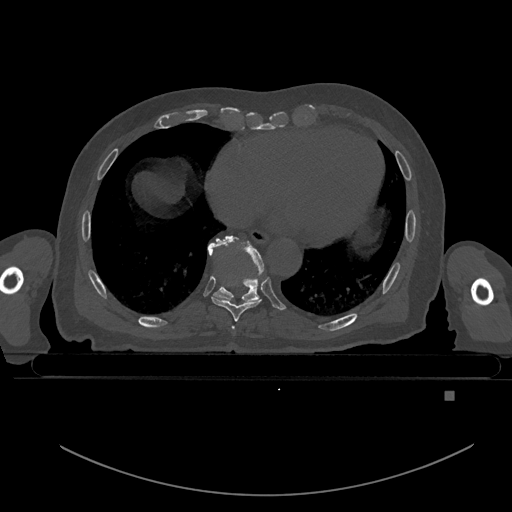
CT including the spine, one axial slice. Bone window (W 1800 / L 400 HU). 0.5 mm slice thickness. 512 × 512 image matrix, field of view 456 × 456 mm. Male patient, age 82 years. From the clinical record (not read from this slice): primary cancer: prostate; vertebrae with lytic lesions (as recorded): T11, T9, T8, T2.
Structures marked on this image (semi-automatically segmented with operator editing):
- T7 vertebra: bounding box <232,327,235,331> (left, top, right, bottom; pixels)
- T8 vertebra: <211,273,262,322>
- T9 vertebra: <207,235,264,303>